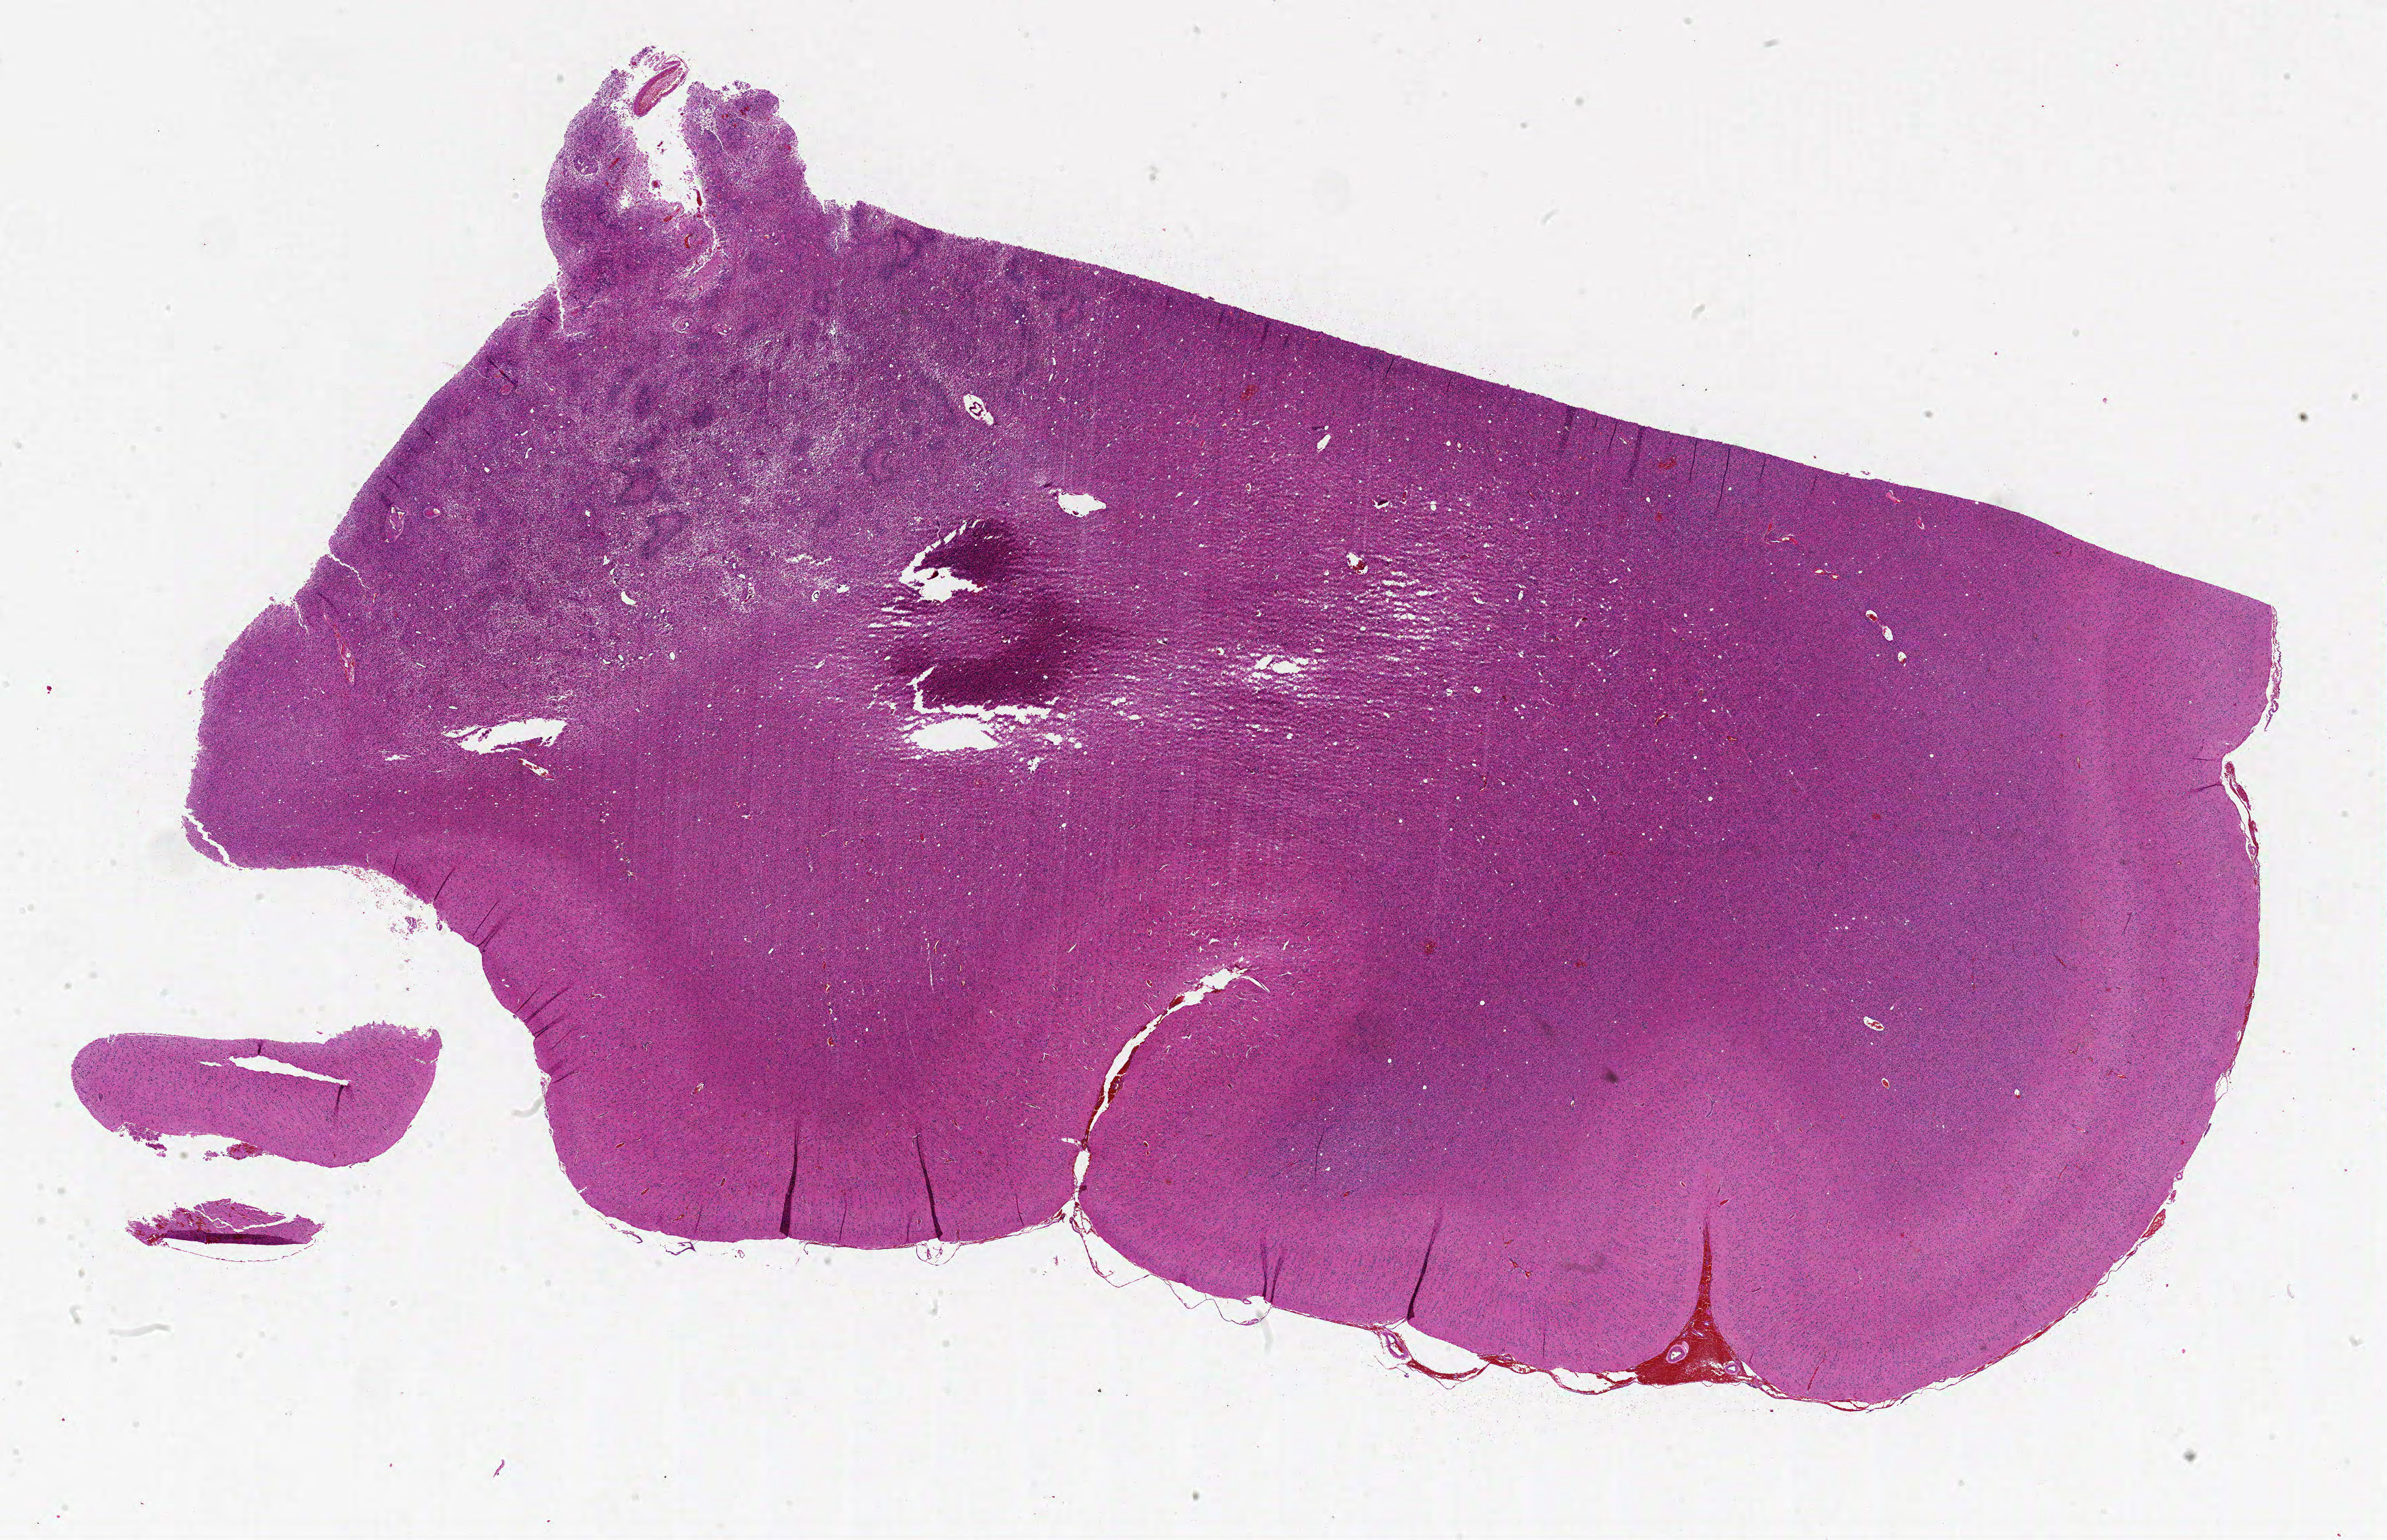
Digitized H&E-stained tissue section (whole slide), whole scanned area (about 28.0 x 18.0 mm) shown as a low-resolution overview; FFPE section; brain, primary tumour sample. Male, age 77 years at initial diagnosis.
Histologic diagnosis: Glioblastoma.